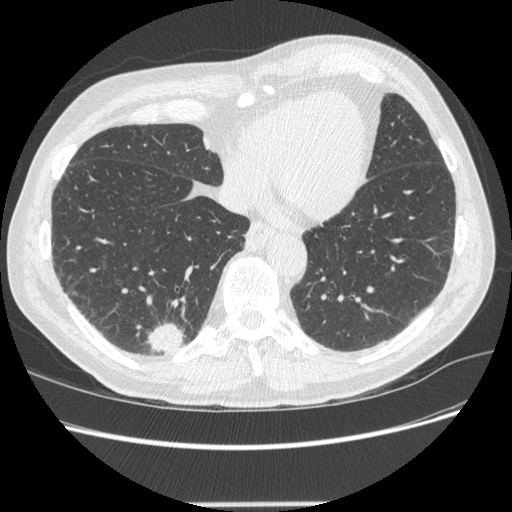
Low-dose screening chest CT, one axial slice. Position 69 of 245 along the scan axis. 120 kVp. Lung window (W 1500 / L -600 HU). 512 × 512 image matrix, field of view 372 × 372 mm.
Annotated regions visible in this slice (outlined manually by an expert reader):
- lesion 1 (tumor, lower lobe of right lung): bounding box <147,322,184,354> (left, top, right, bottom; pixels)